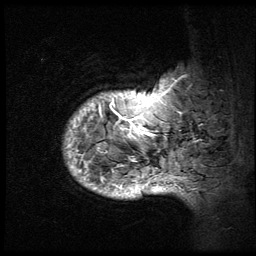
Breast MRI (dynamic contrast-enhanced), one sagittal slice; position 8 of 64 along the scan axis; 3 images stored at this slice position (order not interpretable as contrast timing); 1.5 T; TE 4.2 ms, TR 9 ms; 256 × 256 image matrix, field of view 180 × 180 mm. Female patient, age 50 years. From the clinical record (not read from this slice): setting: breast cancer imaged before/during neoadjuvant chemotherapy; receptor status: triple-negative.
Outlined on this slice (semi-automatic segmentation, software-assisted and operator-edited):
- analysis volume of interest (the breast-tissue region the enhancement analysis was run in; not a lesion): bounding box [x1, y1, x2, y2] px = [62, 59, 194, 210]
- tumour enhancement mask (voxels above the 140 % enhancement threshold inside the analysis volume of interest): [65, 77, 186, 199]